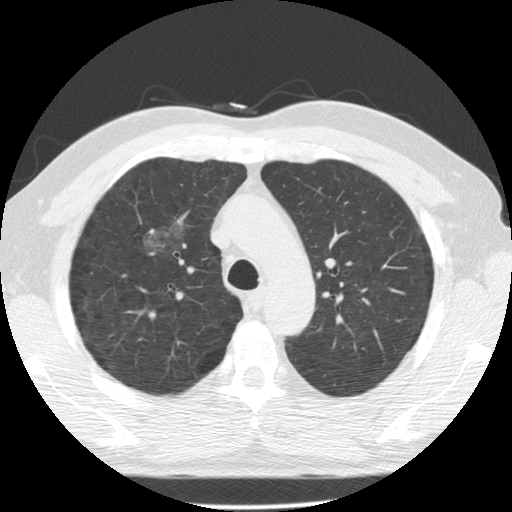
Axial slice from a low-dose chest CT screening exam; second screening round (one year after baseline); lung window (W 1500 / L -600 HU); 2.5 mm slice thickness; standard (soft-tissue) reconstruction kernel (STANDARD); slice 94 of 135 in the series; 512 × 512 image matrix. Male, age 60 years at enrolment. Former smoker at enrolment.
Expert-annotated lung lesion, box from (x=132, y=207) to (x=201, y=270) px. Screening reader's record for this exam (one nodule recorded; not confirmed to be the boxed lesion): non-calcified nodule or mass ≥4 mm, right upper lobe, poorly defined margins, mixed attenuation, pre-existing on the prior screen: yes; interval growth: yes. Participant outcome: lung cancer diagnosed 562 days after this screen — papillary adenocarcinoma, NOS, right upper lobe, moderately differentiated (G2), stage IB (AJCC 6th edition), 32 mm at pathology.